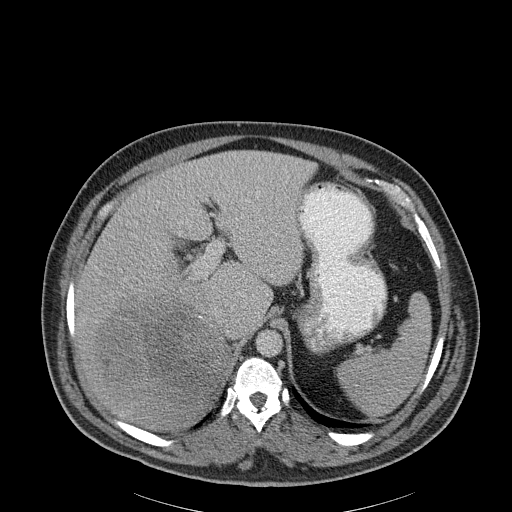
Contrast-enhanced abdominal CT, one axial slice; slice 146 of 186 in the series (ordered by position); reconstruction kernel B30f; soft-tissue window (W 400 / L 40 HU); 512 × 512 image matrix, field of view 464 × 464 mm. Male patient, age 56 years. Case-level facts recorded for this patient, not image findings: diagnosis: adrenocortical carcinoma; tumour side: right adrenal; tumour size at pathology: 18 cm; Ki-67 index: 2 %.
Annotated regions visible in this slice (semi-automatically segmented with operator editing):
- mass: bounding box [x1, y1, x2, y2] px = [100, 300, 222, 405]